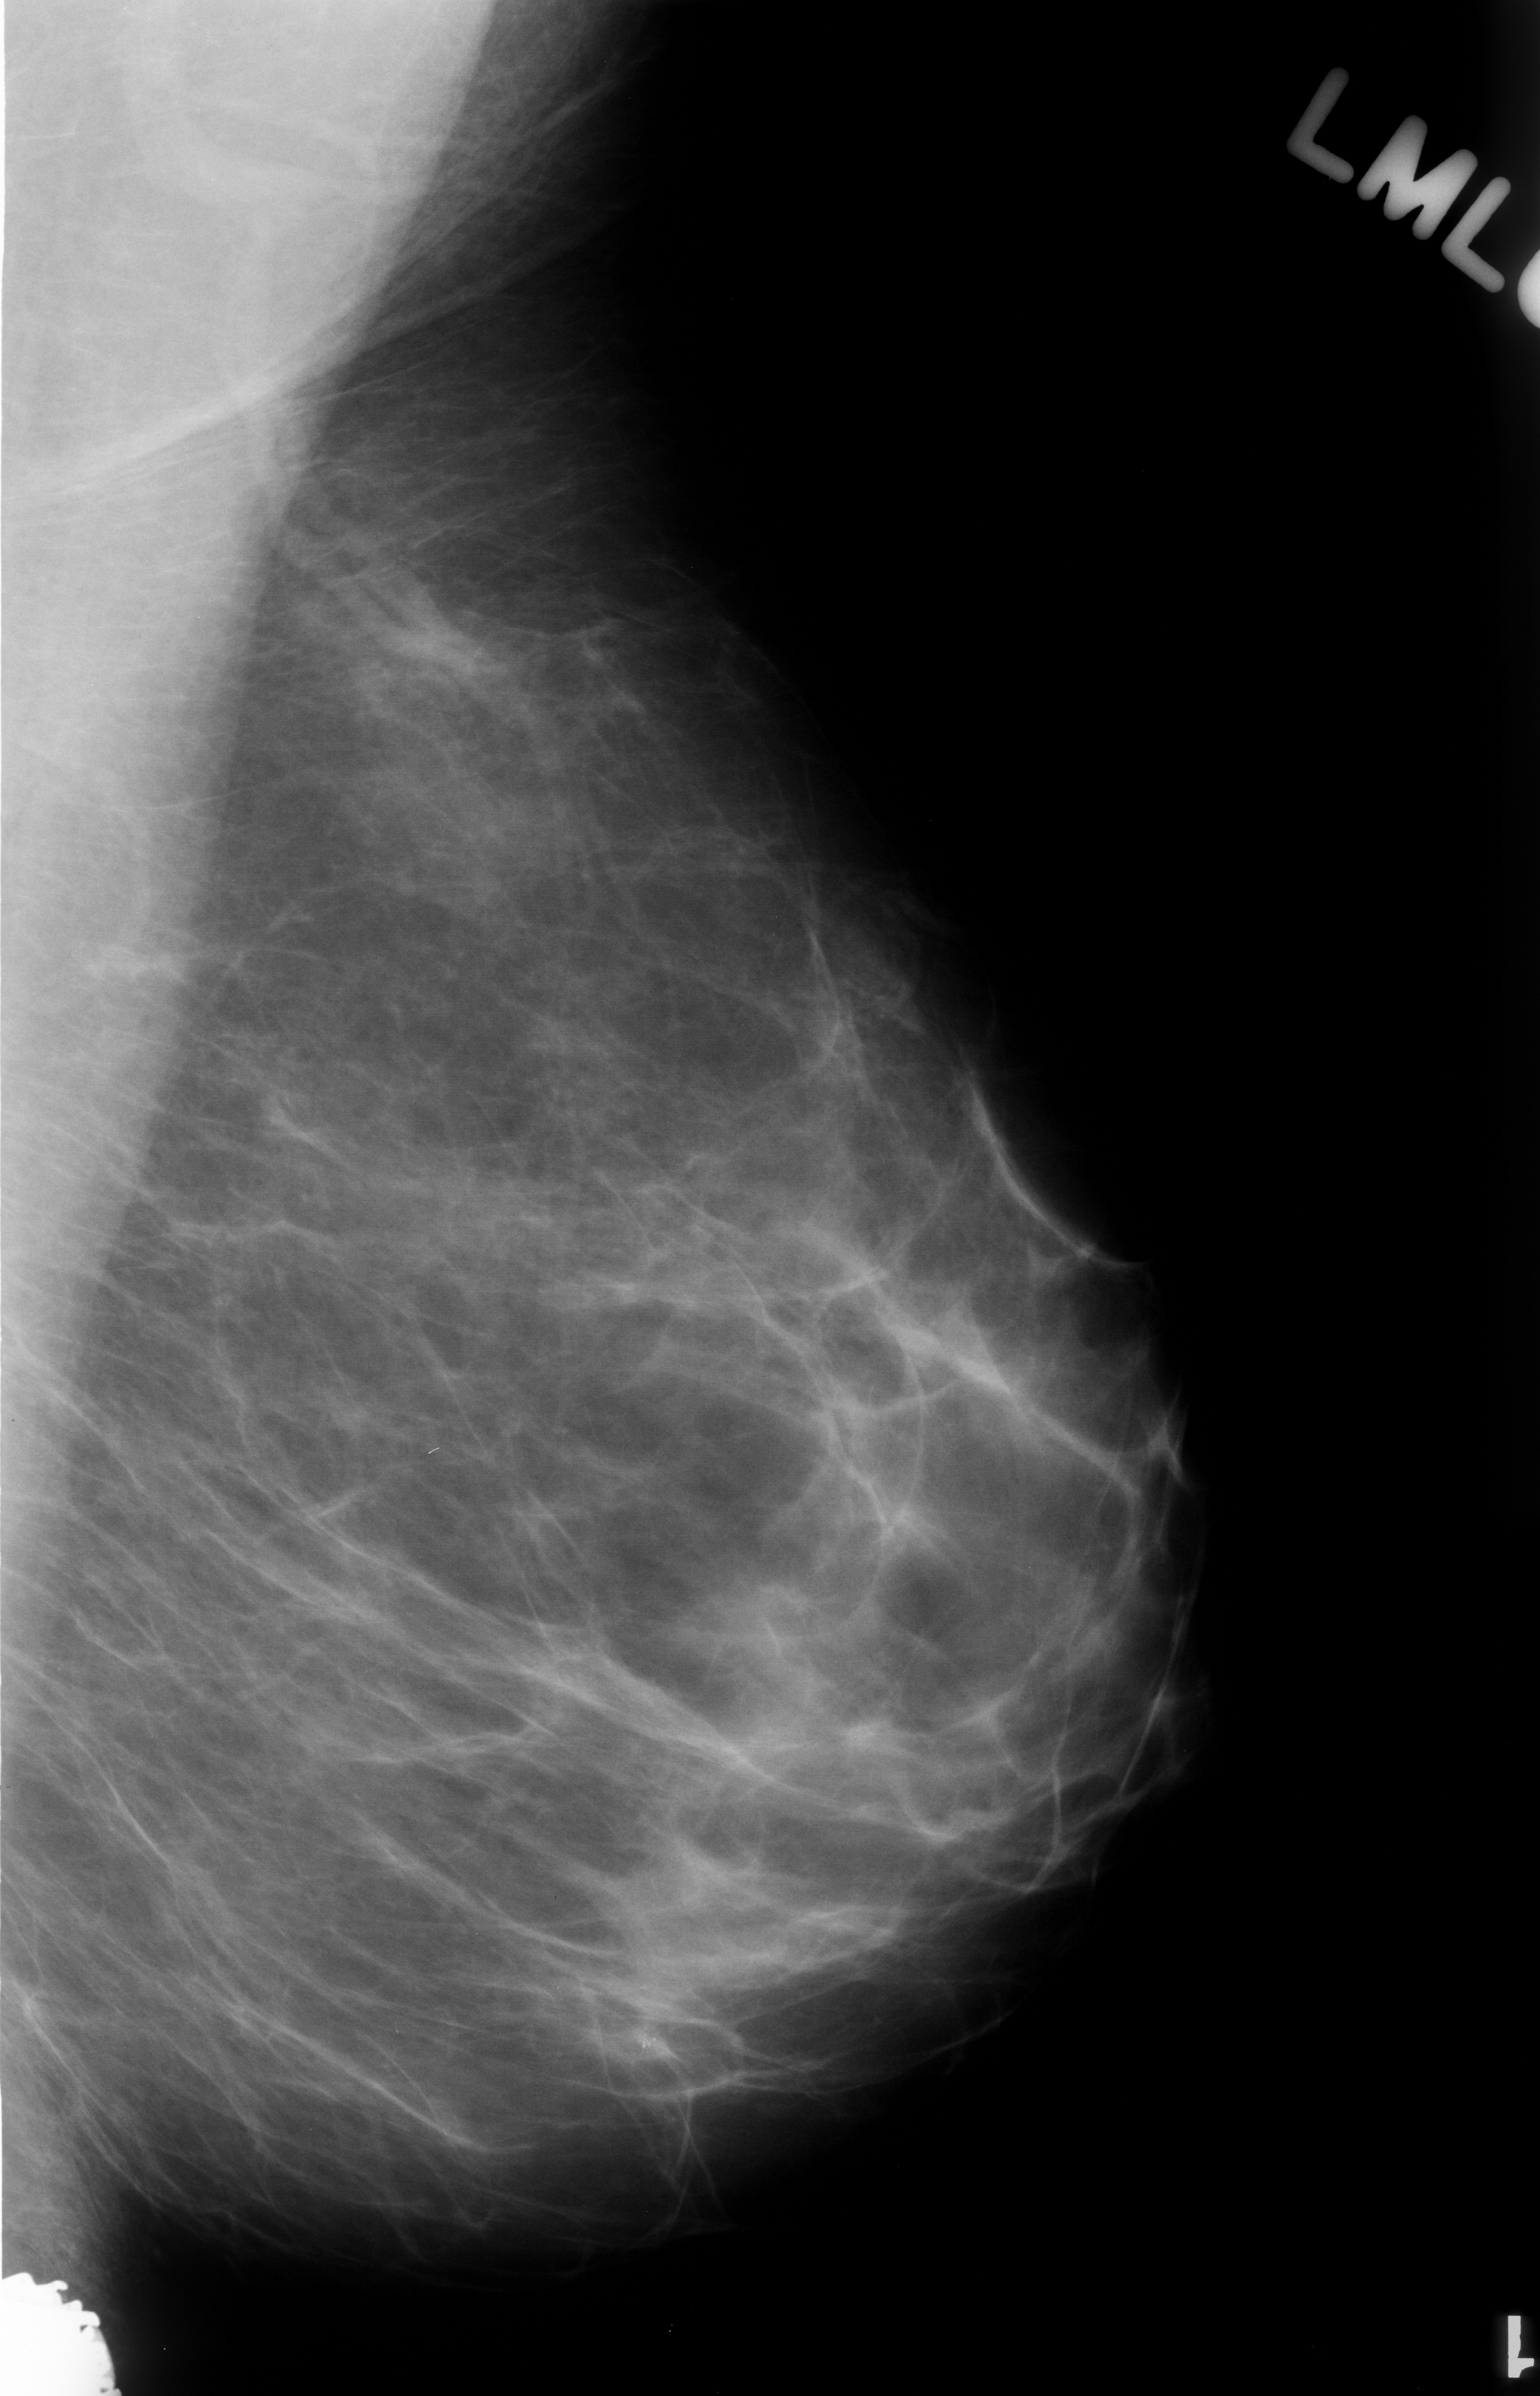
Mammogram (digitized film). Left breast. MLO view. Breast composition: almost entirely fatty (BI-RADS density category 1 of 4). 1540 × 2396 image matrix.
Expert-marked regions of interest on this image (one box per marked abnormality):
- calcifications, morphology pleomorphic, distribution clustered; BI-RADS assessment category 3; subtlety rating 3 on a 1 (subtle) to 5 (obvious) scale; pathology (as recorded): benign: bounding box (x1, y1, x2, y2) in pixels: (564, 1946, 724, 2106)